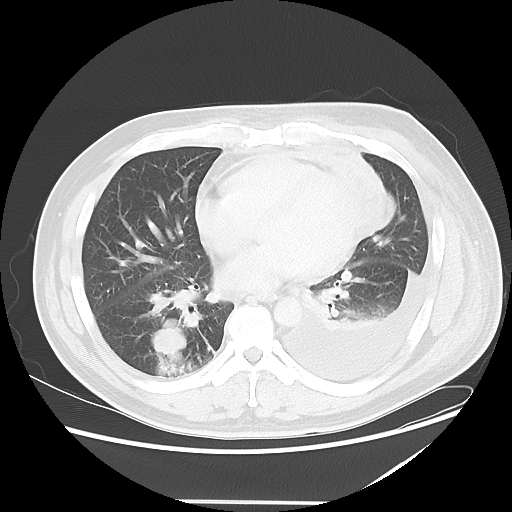
Chest CT, one axial slice. Slice 20 of 52 in the series (ordered by position). Reconstruction kernel LUNG. 120 kVp. Lung window (W 1500 / L -600 HU). 512 × 512 image matrix, field of view 405 × 405 mm. Patient: male, 42 years. From the clinical record (not read from this slice): clinical TNM (as recorded): T2 N1 M1.
Annotated regions visible in this slice (bounding box drawn by a radiologist):
- lung tumour (recorded histology: adenocarcinoma): bounding box [x1, y1, x2, y2] px = [149, 321, 190, 359]